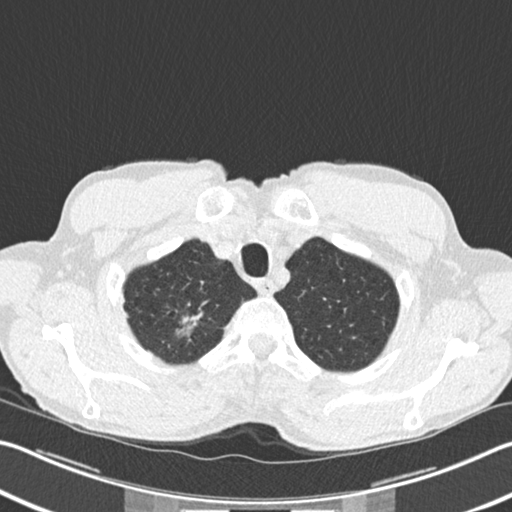
Low-dose screening chest CT, one axial slice; position 197 of 220 along the scan axis; 120 kVp; lung window (W 1500 / L -600 HU); 2 mm slice thickness; 512 × 512 image matrix.
Structures marked on this image (expert manual segmentation):
- lesion 1 (tumor, upper lobe of right lung): bounding box <177,313,202,335> (left, top, right, bottom; pixels)